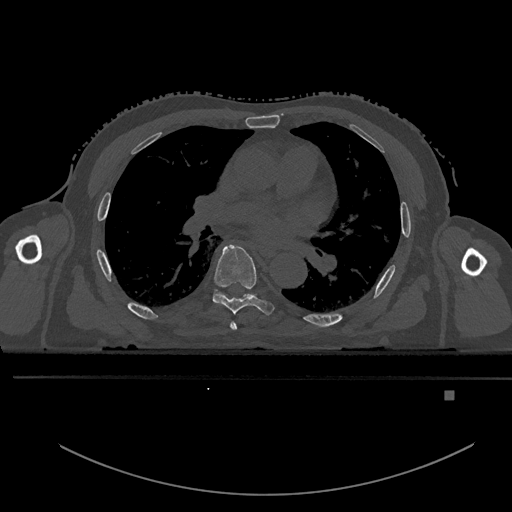
CT including the spine, one axial slice. Position 305 of 969 along the scan axis. Bone window (W 1800 / L 400 HU). 512 × 512 image matrix. Patient: male, 82 years. From the clinical record (not read from this slice): primary cancer: prostate.
Structures marked on this image (semi-automatically segmented with operator editing):
- T5 vertebra: bounding box <230,321,237,331> (left, top, right, bottom; pixels)
- T6 vertebra: <212,245,275,315>